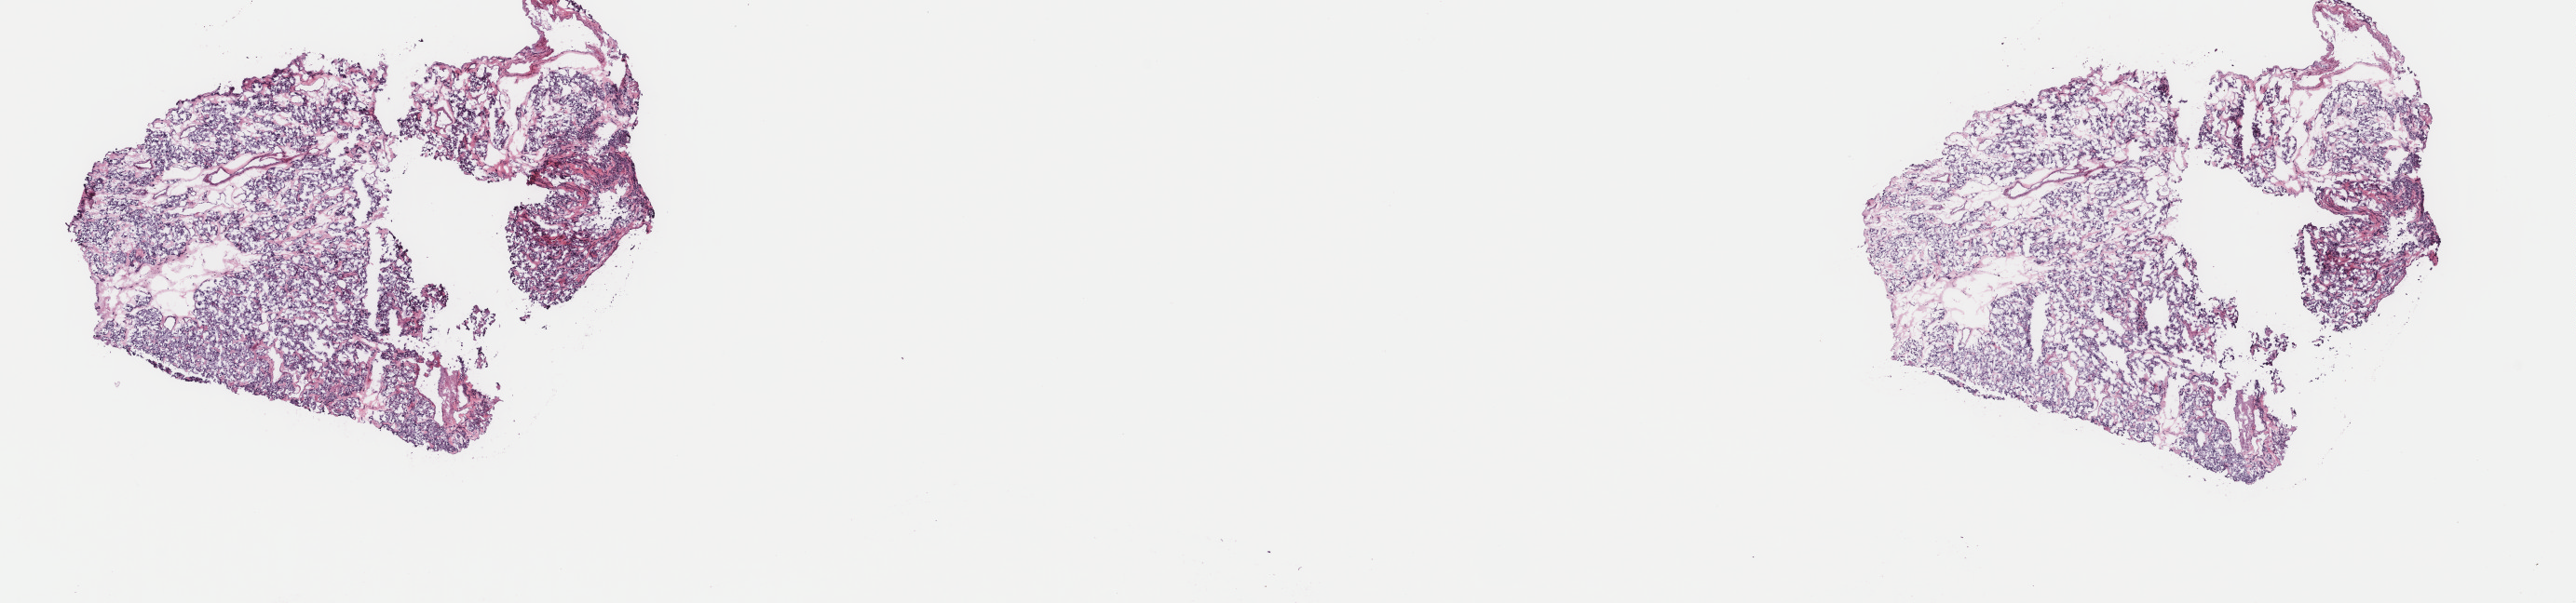
Hematoxylin and eosin (H&E) stained whole-slide image — shown as a low-resolution overview of the whole scanned area (about 22.0 x 5.1 mm), frozen section from the top of the tissue portion, sample: primary tumour, retroperitoneum and peritoneum. Female, age 72 years at initial diagnosis. Slide review estimates, as recorded: tumour cells 100%, tumour nuclei 75%, normal cells 0%, stromal cells 0%, necrosis 0%. Inflammatory infiltration, as recorded: lymphocyte infiltration 1%, monocyte infiltration 0%, neutrophil infiltration 0%.
* histologic diagnosis: Extra-adrenal paraganglioma, NOS